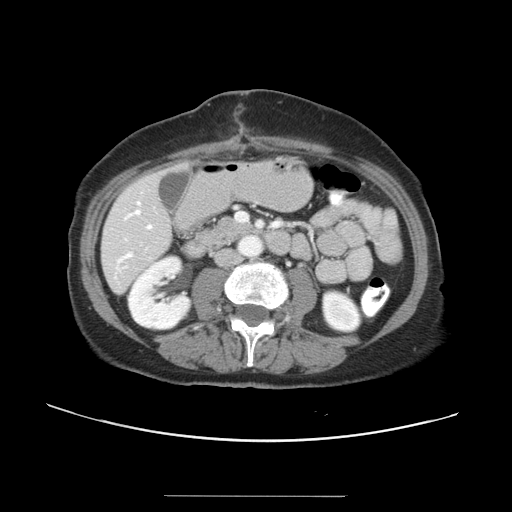
Contrast-enhanced abdominal CT, one axial slice; position 9 of 34 along the scan axis; reconstruction kernel STANDARD; 120 kVp; intravenous contrast given; soft-tissue window (W 400 / L 40 HU); 5 mm slice thickness; 512 × 512 image matrix, field of view 382 × 382 mm. Female patient, age 69 years. From the clinical record (not read from this slice): diagnosis: colorectal cancer liver metastases, imaged before liver resection; multiple liver metastases: yes; largest metastasis: 1.4 cm; disease in both lobes: yes.
Outlined on this slice (expert manual segmentation):
- hepatic veins: bounding box [x1, y1, x2, y2] px = [116, 201, 141, 271]
- liver: [102, 170, 172, 293]
- planned liver remnant (the part of the liver to remain after resection): [102, 169, 177, 293]
- portal vein (with intrahepatic branches): [146, 212, 279, 229]